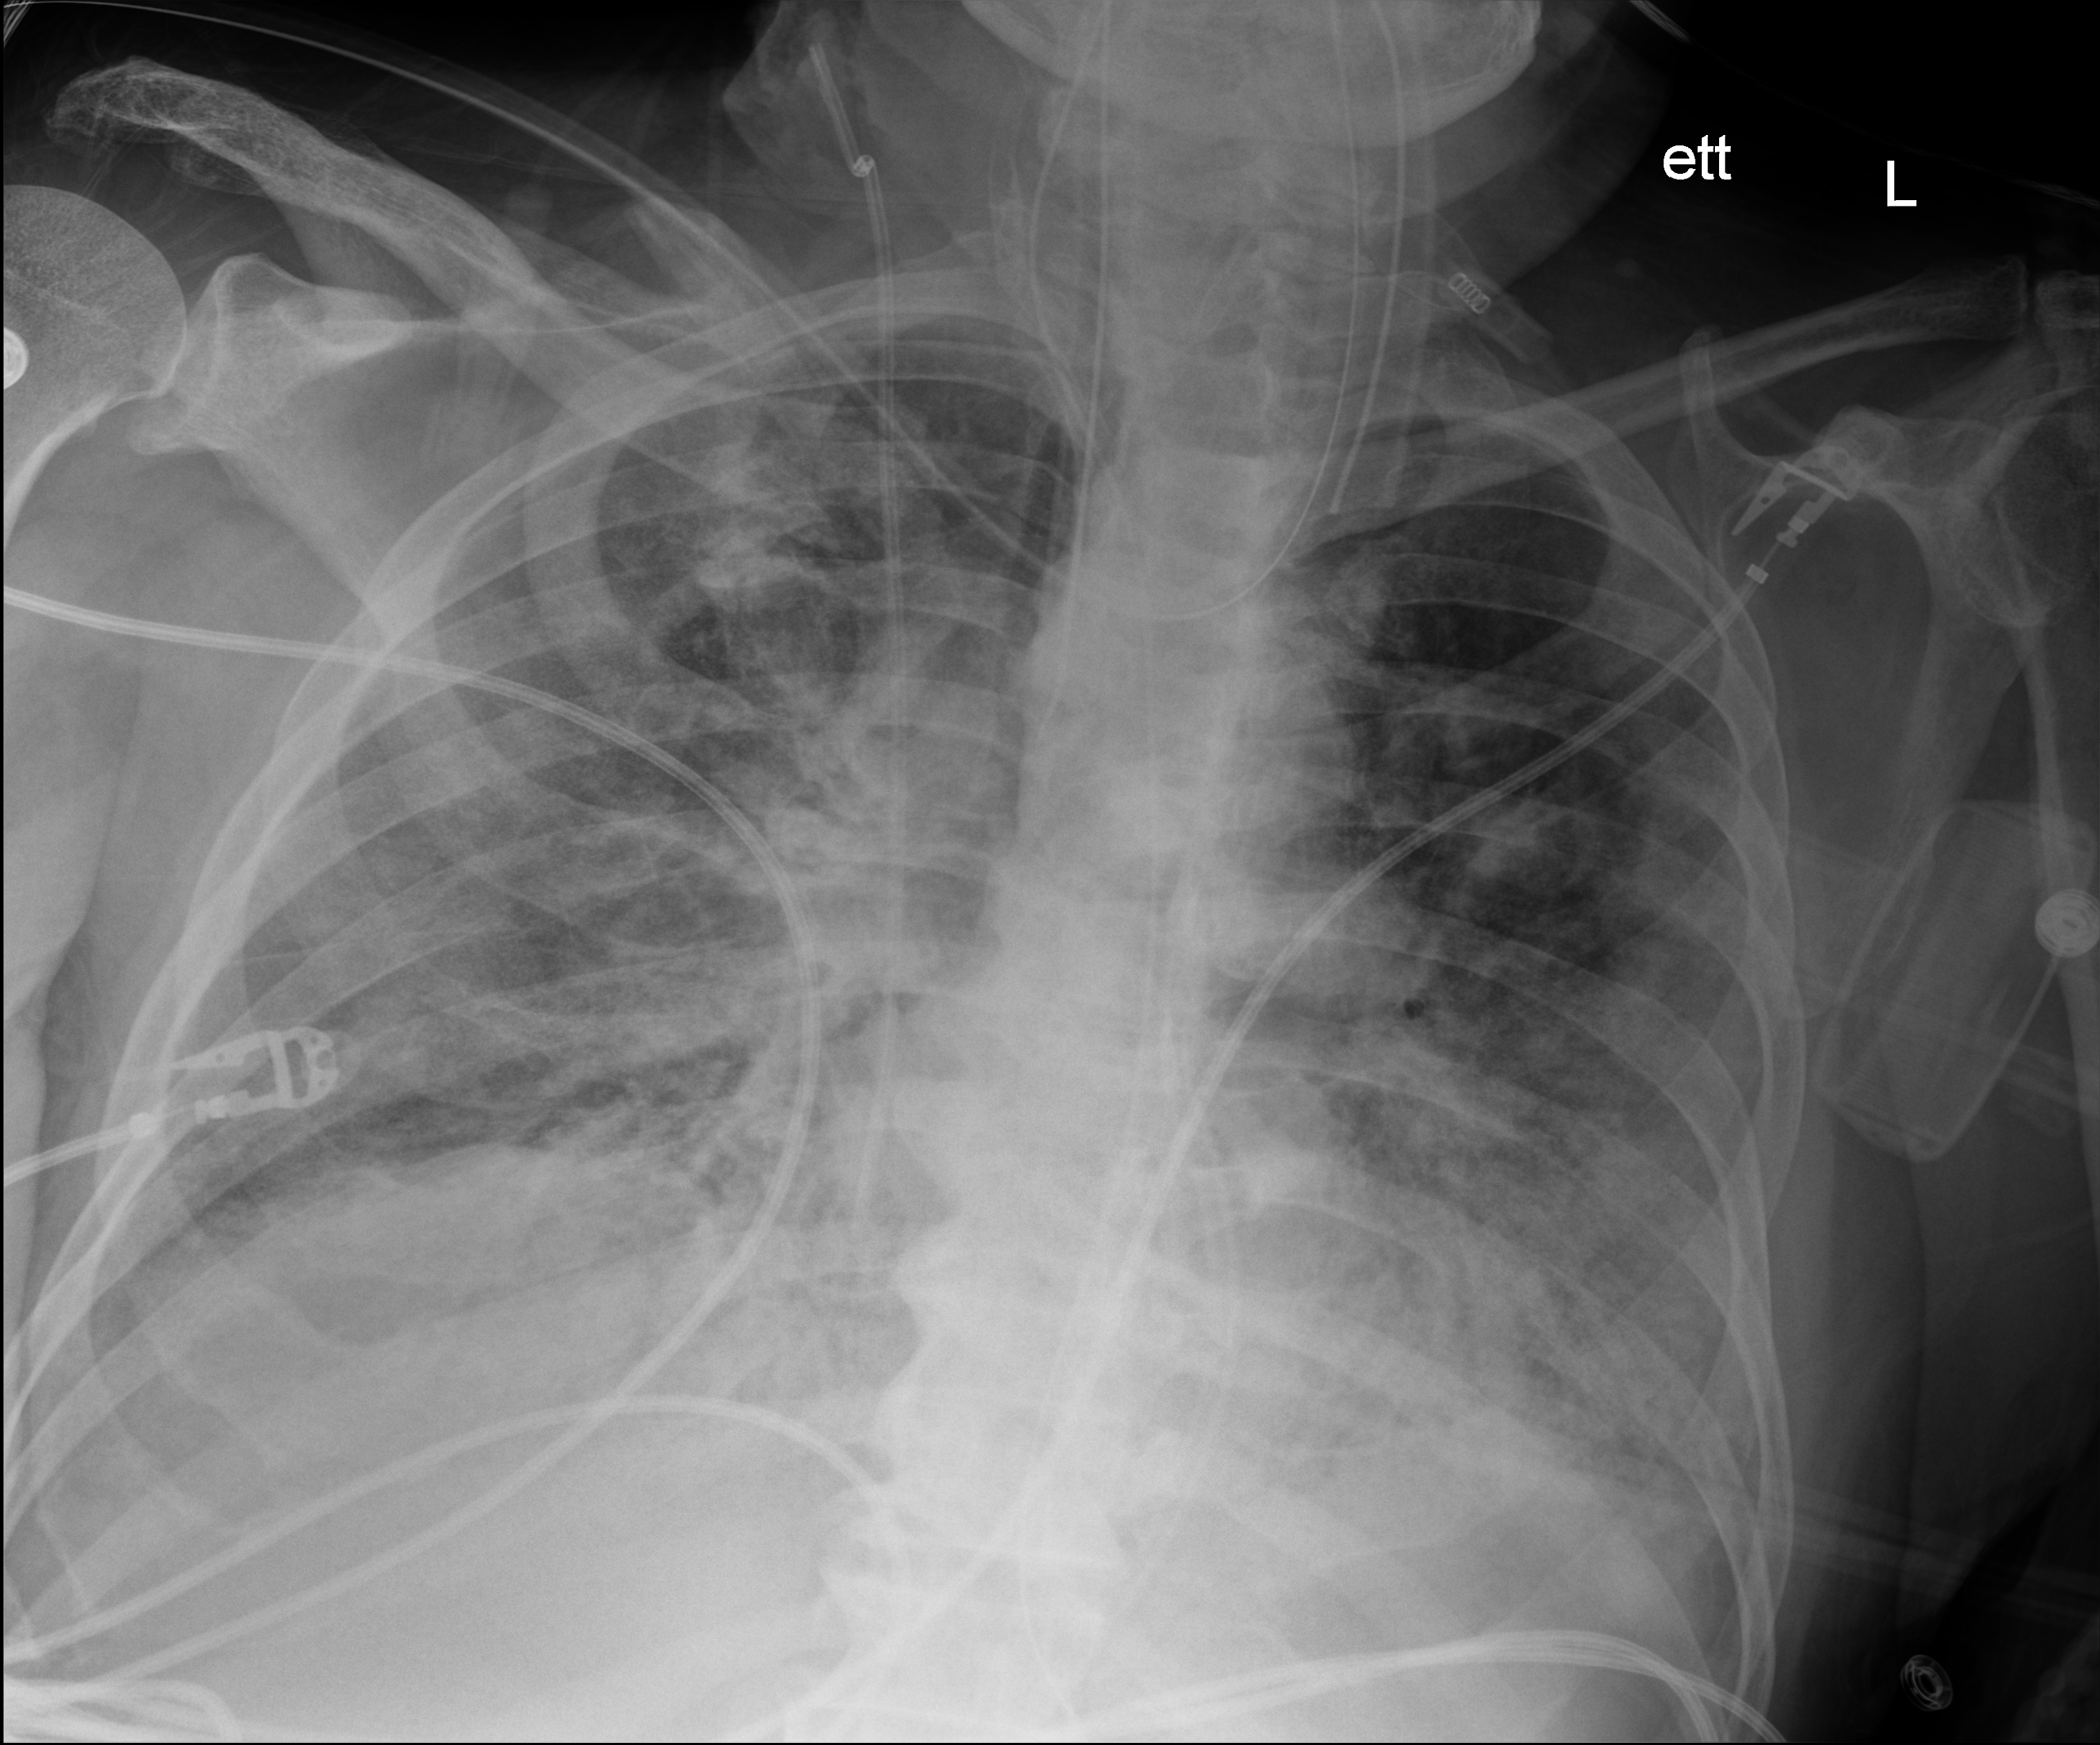
Portable chest radiograph; anteroposterior (AP) projection. Male patient hospitalised with COVID-19, age 75–90 years.
Admission-level facts for this patient (not findings on this image; timing relative to this image not recorded): mechanically ventilated during this hospital stay: yes; smoking status (admission record): former.